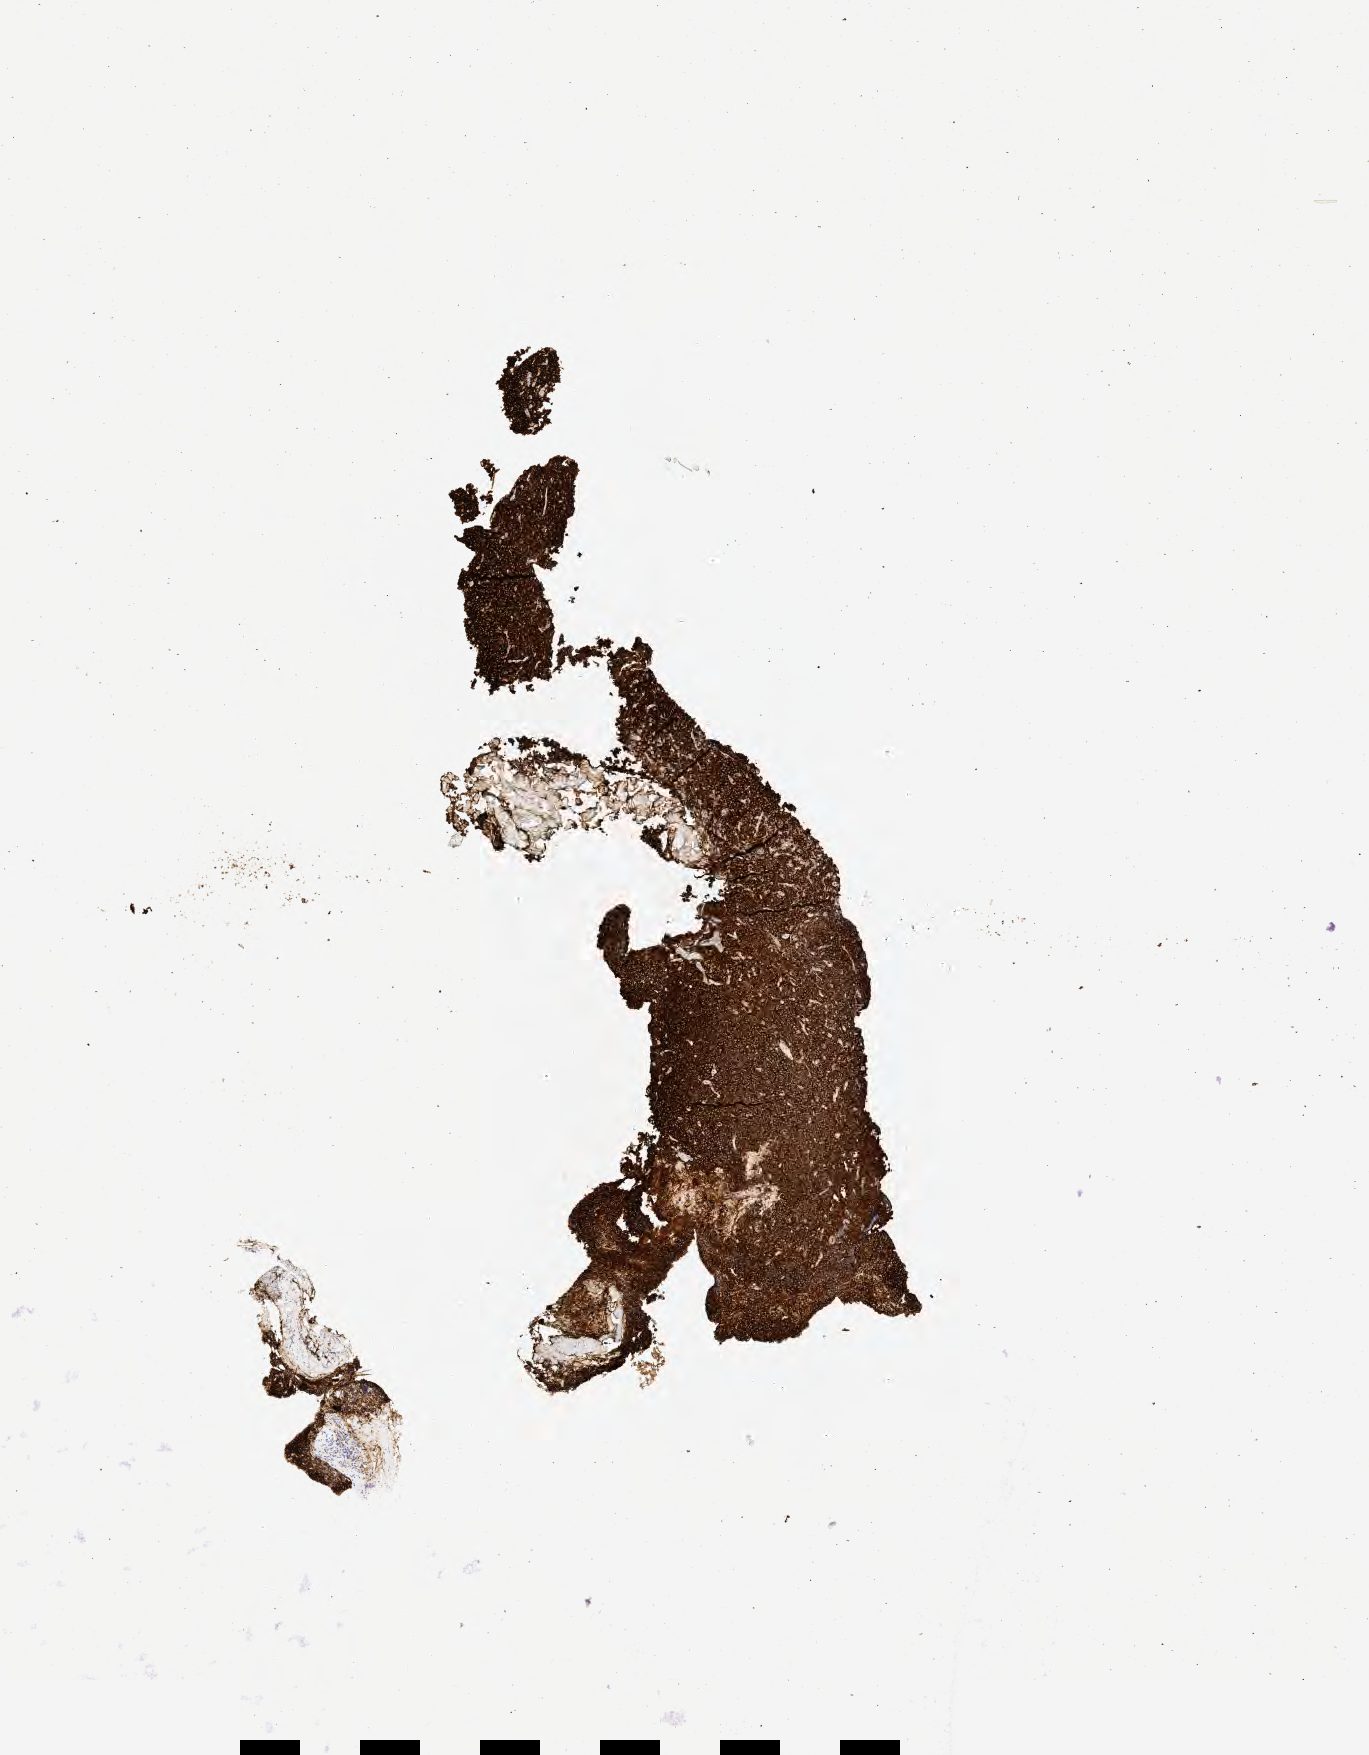
Immunohistochemistry (IHC) whole-slide image stained for CD20, shown as a low-resolution overview of the whole scanned area (about 5.5 x 7.1 mm). Specimen: tumor tissue. Female patient, age 27 years.
Histologic diagnosis: Diffuse large B-cell lymphoma, NOS.